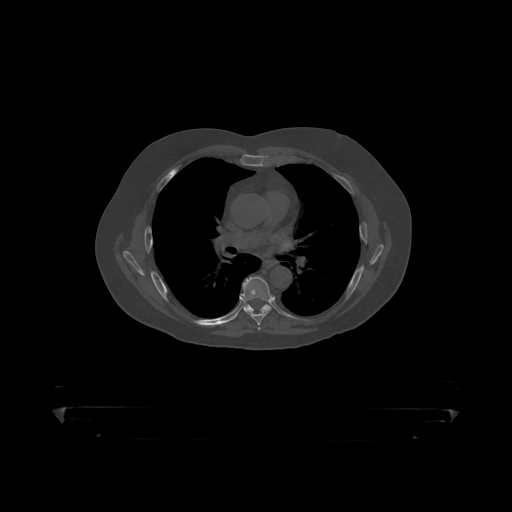
CT including the spine, one axial slice. Reconstruction kernel STANDARD. Bone window (W 1800 / L 400 HU). 1.25 mm slice thickness. 512 × 512 image matrix, field of view 650 × 650 mm. Patient: male, 60 years. Case-level facts recorded for this patient, not image findings: primary cancer: prostate.
Annotated regions visible in this slice (semi-automatic segmentation, software-assisted and operator-edited):
- T6 vertebra: bounding box (x1, y1, x2, y2) in pixels: (241, 277, 273, 319)
- T7 vertebra: (244, 304, 271, 312)